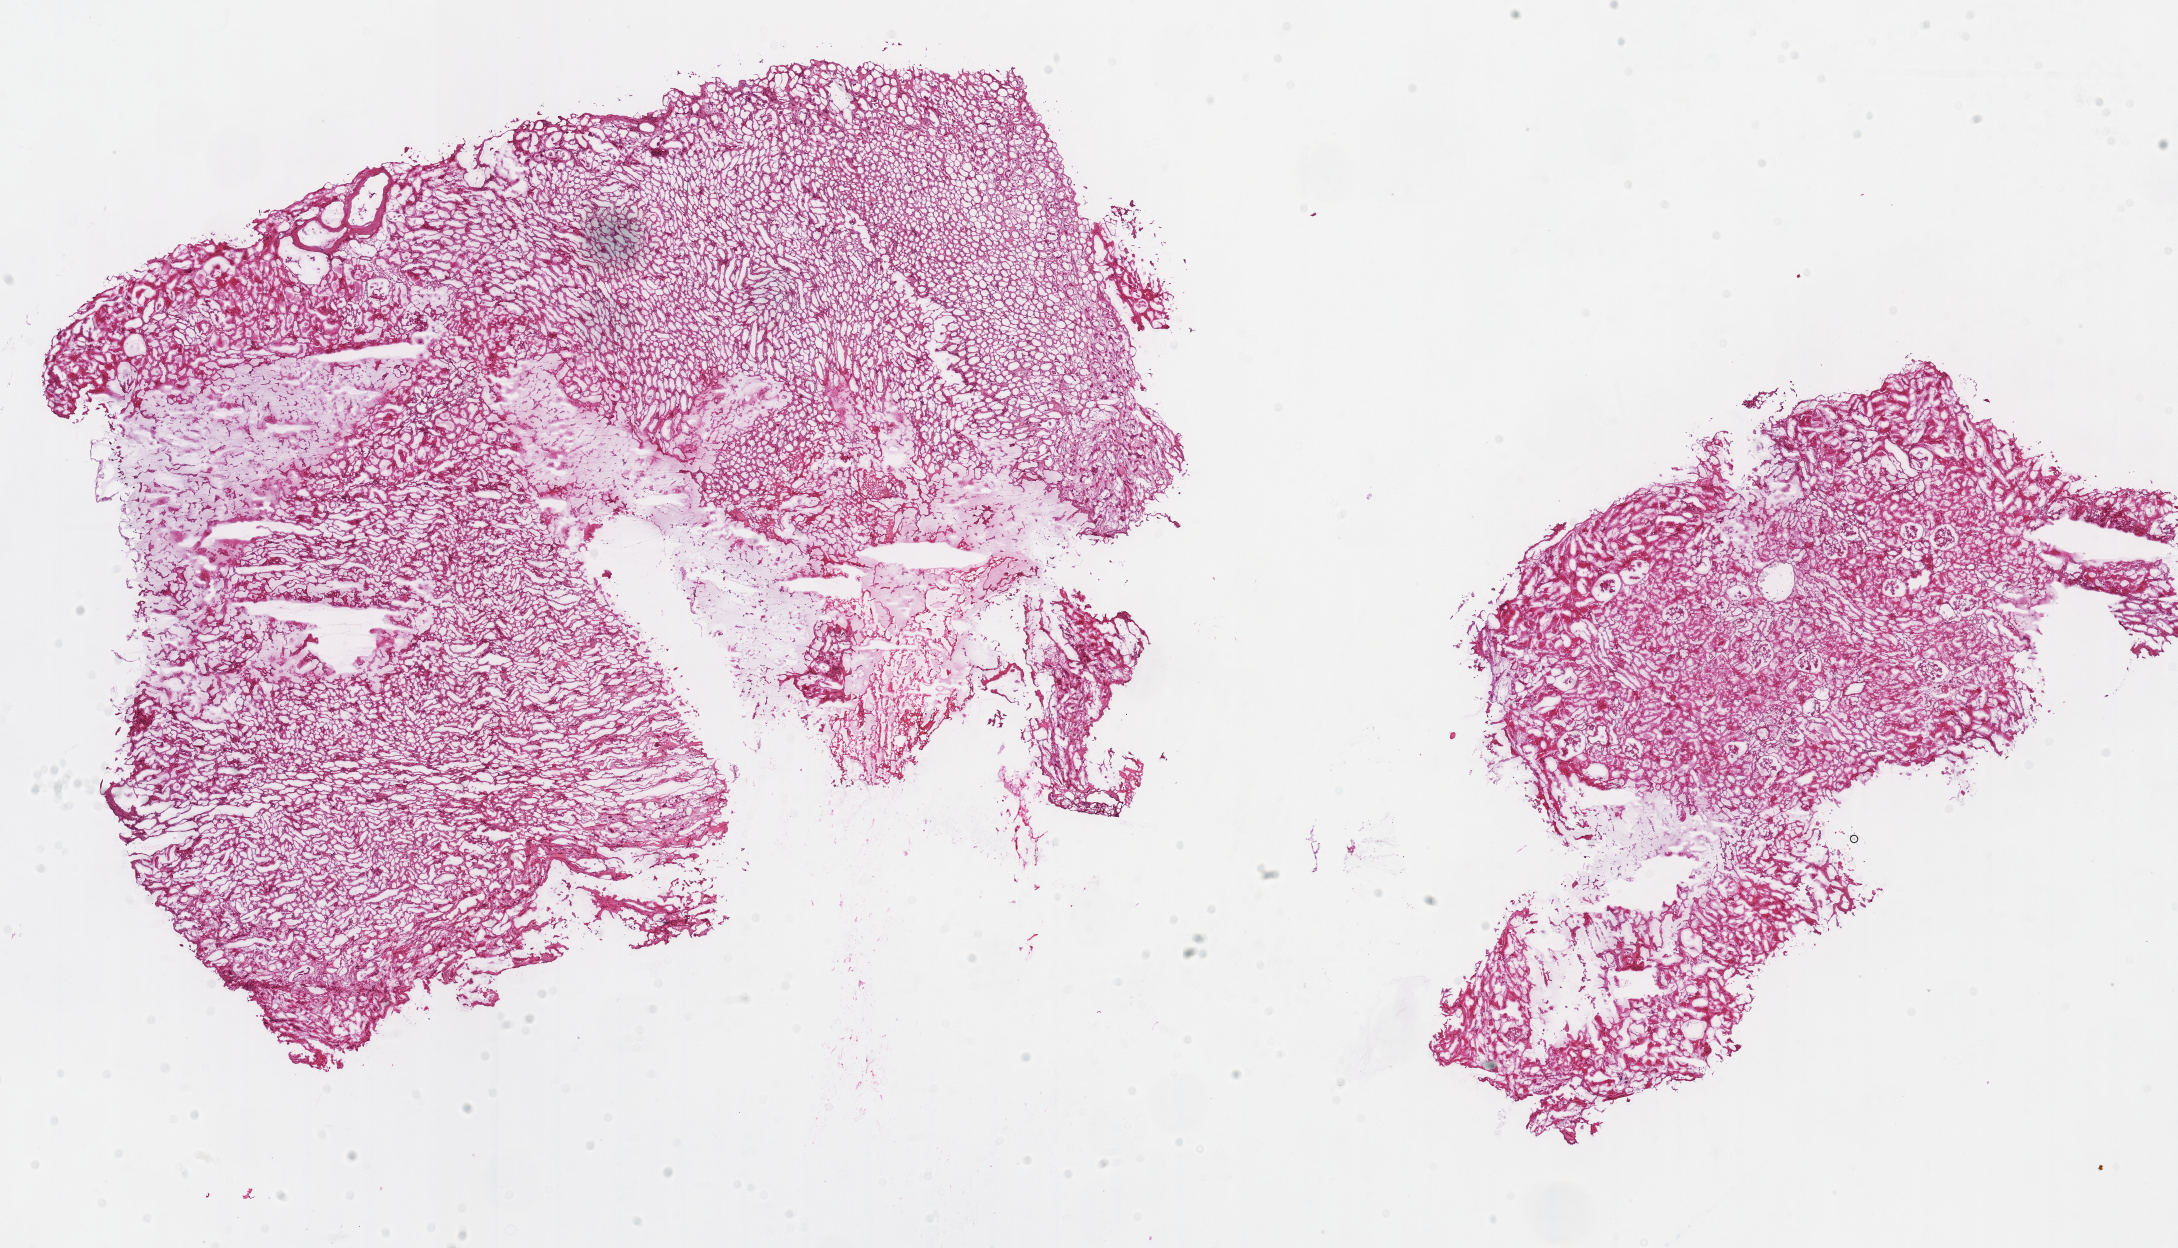
H&E whole-slide image — shown as a low-resolution overview of the whole scanned area (about 17.1 x 9.8 mm, from a 40x scan); frozen section; kidney, solid tissue normal (non-tumour tissue) sample. Female patient; age at initial diagnosis 74 years.
* this section: solid tissue normal (non-tumour) sample from the same patient
* patient diagnosis: Renal cell carcinoma, chromophobe type